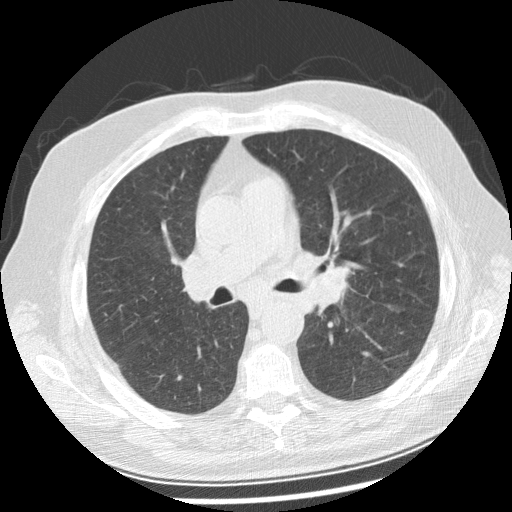
Low-dose screening chest CT, one axial slice; slice 147 of 250 in the series (ordered by position); 120 kVp; lung window (W 1500 / L -600 HU); 2.5 mm slice thickness; 512 × 512 image matrix, field of view 360 × 360 mm.
Outlined on this slice (manually delineated by an expert):
- lesion 1 (tumor, left main bronchus): bounding box <309,267,352,315> (left, top, right, bottom; pixels)